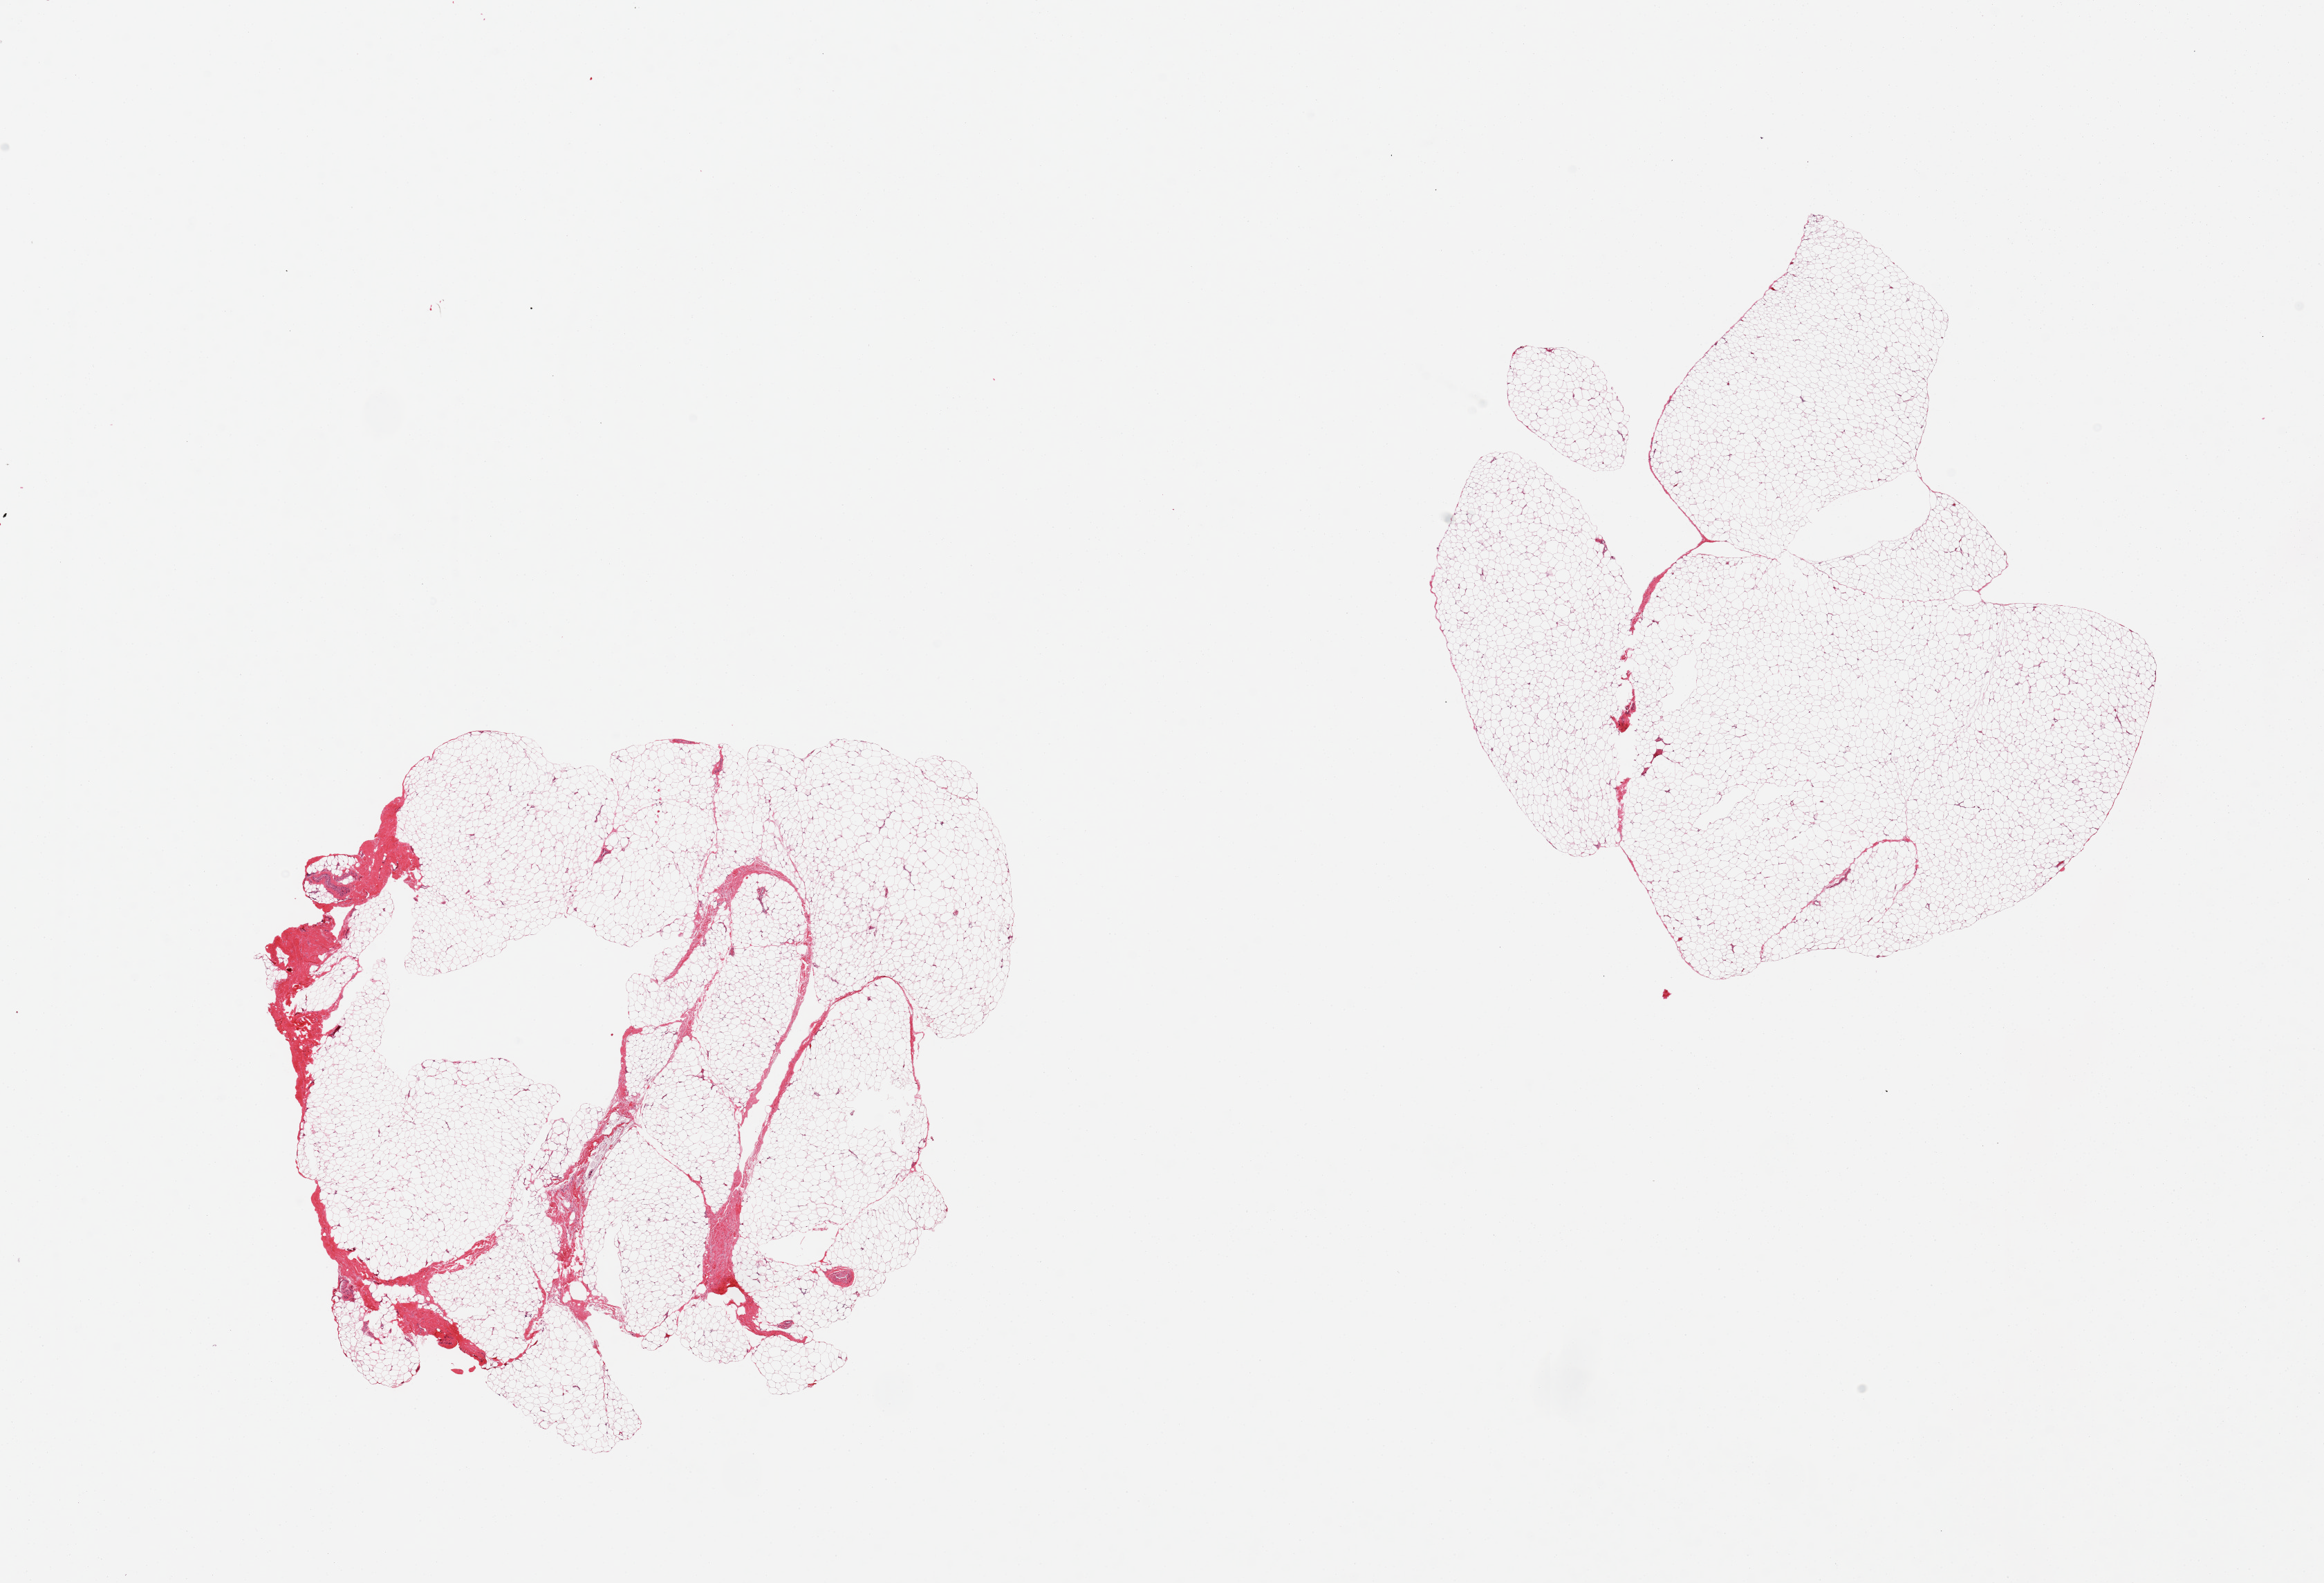
Digitized hematoxylin and eosin (H&E)-stained section, brightfield — shown as a low-resolution overview of the whole scanned area (about 26.6 x 18.1 mm, slide scanned at 20x), PAXgene-fixed, paraffin-embedded tissue, sampled site (target tissue): adipose tissue, donor tissue sample. Donor sex: male.
Reviewer comment on this tissue sample: 2 pieces.